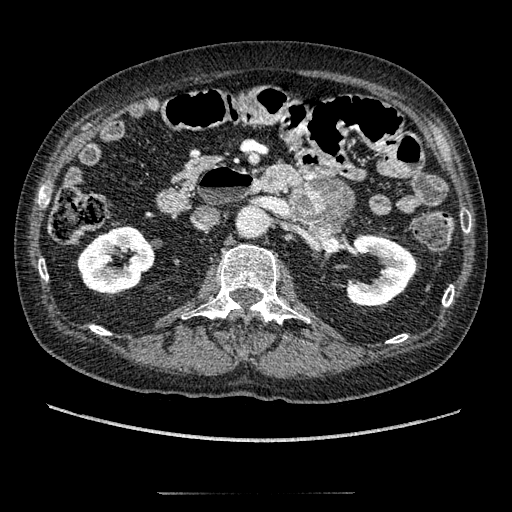
Contrast-enhanced abdominal CT, one axial slice. Slice 88 of 274 in the series (ordered by position). Reconstruction kernel STANDARD. 120 kVp. Soft-tissue window (W 400 / L 40 HU). 1.25 mm slice thickness. 512 × 512 image matrix. Patient: male, 69 years. From the clinical record (not read from this slice): diagnosis: adrenocortical carcinoma; tumour side: left adrenal; tumour size at pathology: 6.1 cm; Ki-67 index: 10 %; stage (as recorded): 3.
Annotated regions visible in this slice (semi-automatically segmented with operator editing):
- mass: bounding box [x1, y1, x2, y2] px = [295, 182, 351, 229]